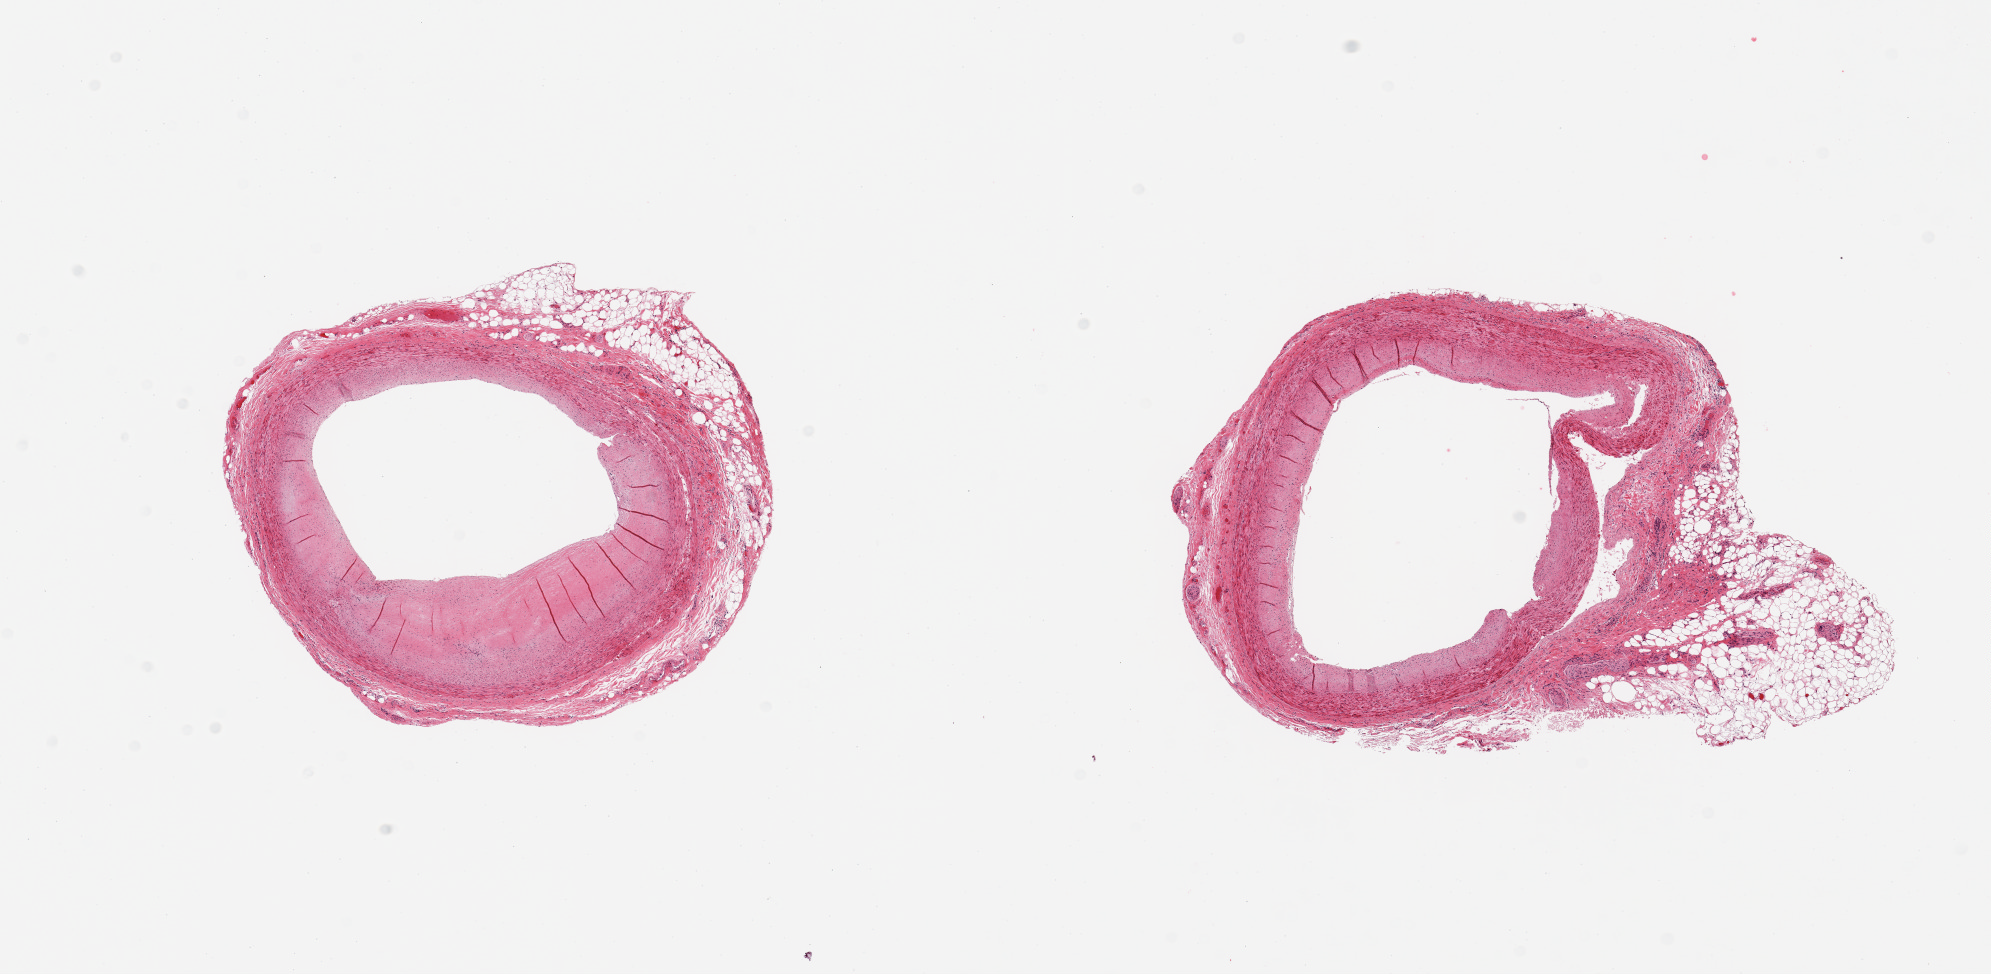
Haematoxylin and eosin whole-slide image, low-resolution overview of the scanned area, about 15.8 x 7.7 mm (acquisition: 20x scan); PAXgene-fixed, paraffin-embedded tissue; target tissue: coronary artery; tissue donor sample. Male donor.
Pathologist's review note for this sample: 2 pieces; eccentric plaque; up to 2 mm external fat.